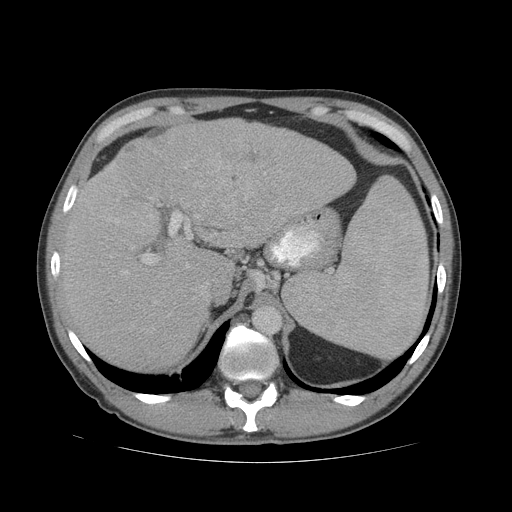
Contrast-enhanced abdominal CT (liver protocol), one axial slice; slice 49 of 81 in the series (ordered by position); reconstruction kernel STANDARD; 140 kVp; soft-tissue window (W 400 / L 40 HU); 2.5 mm slice thickness; 512 × 512 image matrix, field of view 400 × 400 mm. From the clinical record (not read from this slice): diagnosis: hepatocellular carcinoma (patient treated with transarterial chemoembolisation; whether this scan precedes or follows treatment is not stated here); TNM stage (as recorded): Stage-IVB; Child-Pugh class: B; tumour nodularity: multinodular.
Outlined on this slice (semi-automatically segmented with operator editing):
- liver parenchyma outside the tumour (the mass and vessels are separate outlines, so this box may not span the whole liver): box from (x=60, y=118) to (x=356, y=370) px
- mass: (x=109, y=123)–(x=247, y=219)
- liver vessels: (x=115, y=167)–(x=277, y=274)